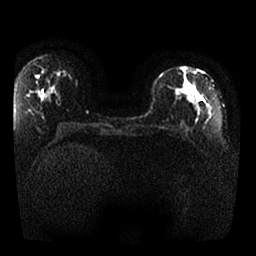
Breast MRI, one axial slice. Diffusion-weighted series; image 2 of 4 stored at this slice position (different b-values; order by instance number). 1.5 T. 256 × 256 image matrix. Female patient.
Outlined on this slice (expert manual segmentation):
- tumour on diffusion-weighted imaging: bounding box [x1, y1, x2, y2] px = [173, 83, 200, 112]